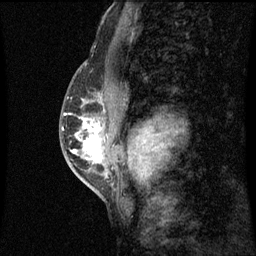
Breast MRI (dynamic contrast-enhanced), one sagittal slice; position 33 of 60 along the scan axis; dynamic contrast-enhanced series, image 2 of 3 at this slice position (ordered by acquisition); 1.5 T; TE 4.2 ms, TR 8.9 ms; 2 mm slice thickness; 256 × 256 image matrix. Female patient, age 50 years. Case-level facts recorded for this patient, not image findings: setting: breast cancer imaged before/during neoadjuvant chemotherapy; receptor status: triple-negative.
Structures marked on this image (semi-automatically segmented with operator editing):
- analysis volume of interest (the breast-tissue region the enhancement analysis was run in; not a lesion): bounding box <68,82,105,169> (left, top, right, bottom; pixels)
- tumour enhancement mask (voxels above the 70 % enhancement threshold inside the analysis volume of interest): <74,118,101,163>